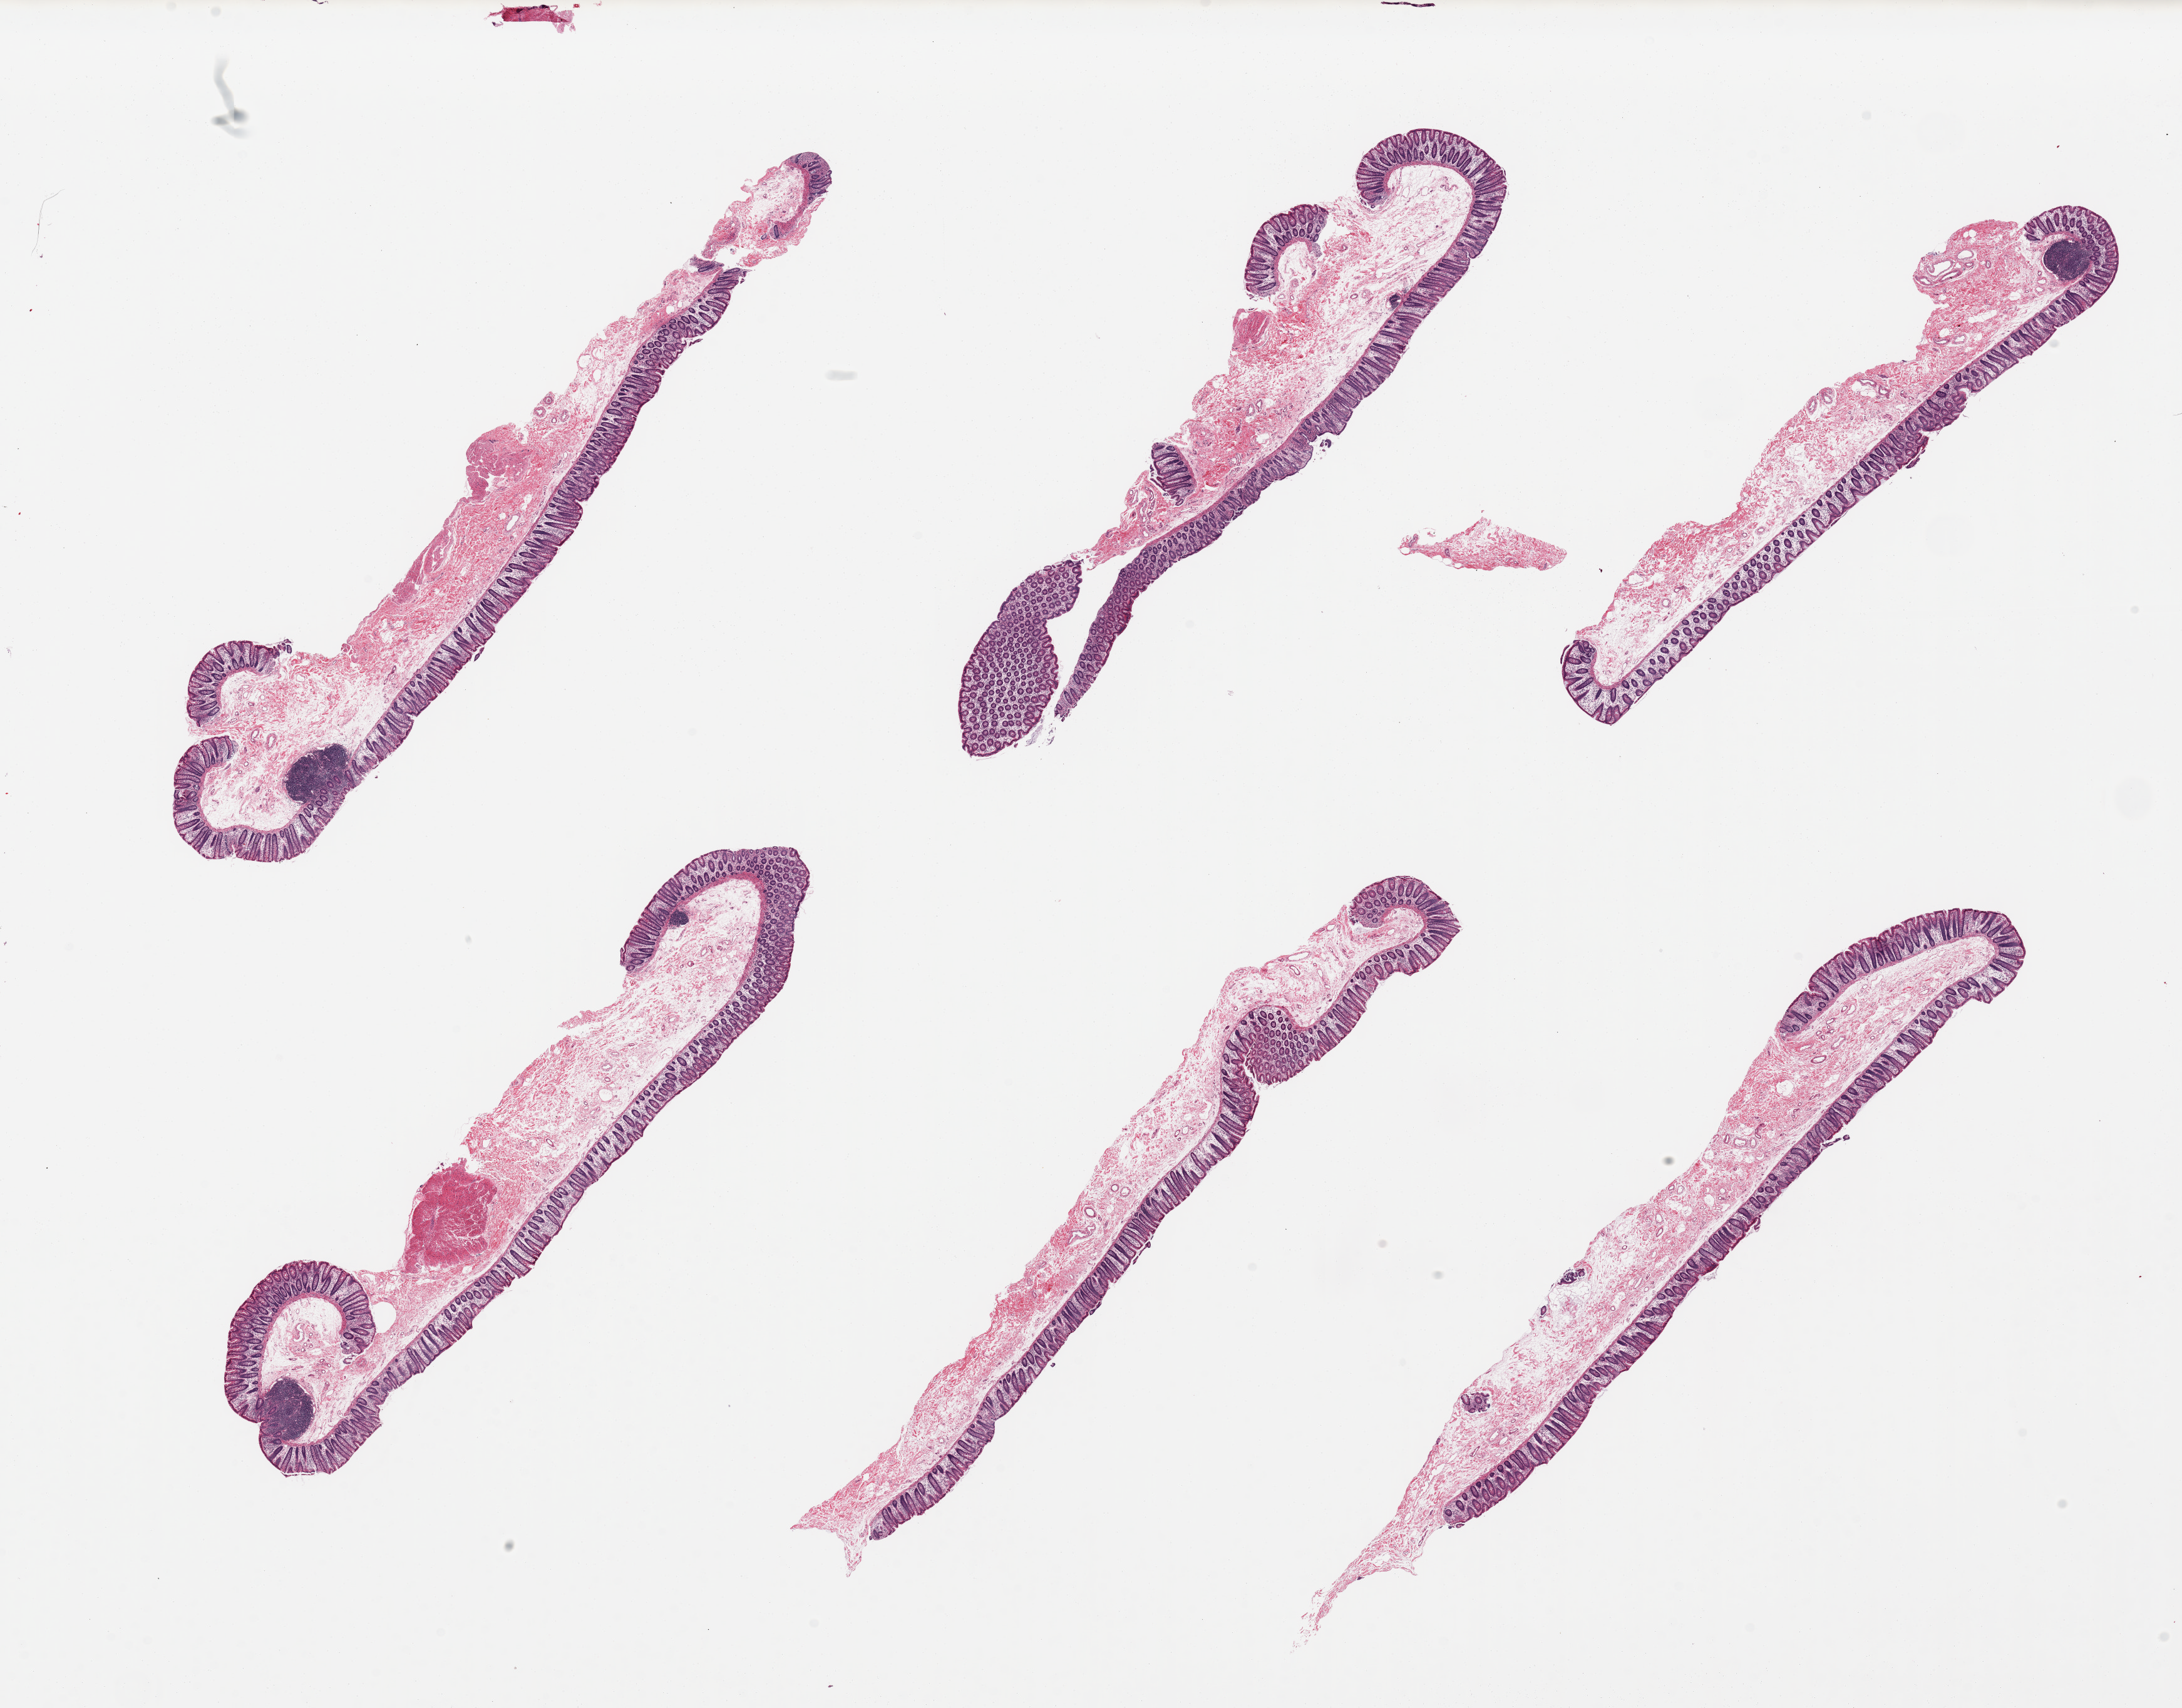
Hematoxylin and eosin (H&E) whole-slide image, shown as a low-resolution overview of the whole scanned area (about 27.6 x 21.6 mm, from a 20x scan). PAXgene-fixed paraffin-embedded (PFPE) section. Sampled site (target tissue): transverse colon. Donor tissue sample. Donor: female.
Reviewer comment on this tissue sample: 6 pieces, well preserved; mucosa up to ~0.3mm, ~20% thickness.